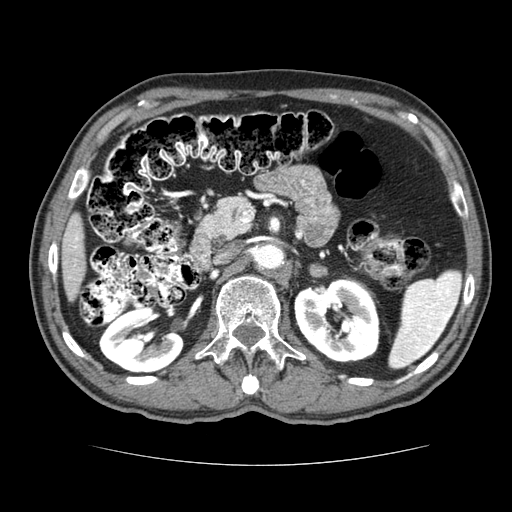
Contrast-enhanced abdominal CT (liver protocol), one axial slice. Position 30 of 79 along the scan axis. Reconstruction kernel STANDARD. Soft-tissue window (W 400 / L 40 HU). 2.5 mm slice thickness. 512 × 512 image matrix, field of view 360 × 360 mm. From the clinical record (not read from this slice): diagnosis: hepatocellular carcinoma (patient treated with transarterial chemoembolisation; whether this scan precedes or follows treatment is not stated here); TNM stage (as recorded): Stage-I; Child-Pugh class: A.
Structures marked on this image (semi-automatic segmentation, software-assisted and operator-edited):
- liver parenchyma outside the tumour (the mass and vessels are separate outlines, so this box may not span the whole liver): bounding box [x1, y1, x2, y2] px = [62, 212, 84, 300]
- liver vessels: [73, 233, 79, 249]